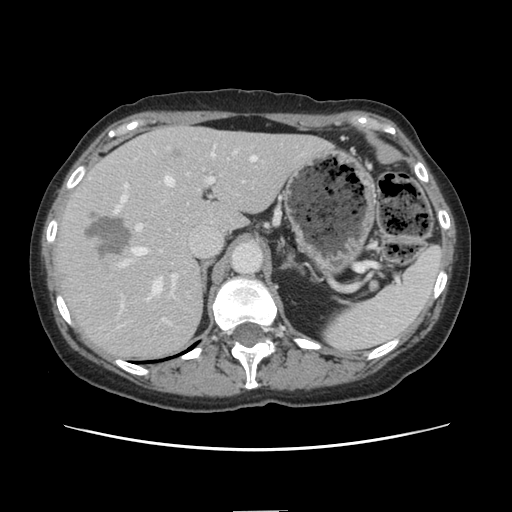
Contrast-enhanced abdominal CT, one axial slice; slice 95 of 141 in the series (ordered by position); intravenous contrast given; soft-tissue window (W 400 / L 40 HU); 2.5 mm slice thickness; 512 × 512 image matrix. Female patient, age 63 years. From the clinical record (not read from this slice): diagnosis: colorectal cancer liver metastases, imaged before liver resection; multiple liver metastases: yes; largest metastasis: 3.2 cm.
Outlined on this slice (expert manual segmentation):
- hepatic veins: bounding box [x1, y1, x2, y2] px = [123, 152, 256, 300]
- liver: [54, 128, 329, 360]
- planned liver remnant (the part of the liver to remain after resection): [183, 128, 328, 235]
- portal vein (with intrahepatic branches): [114, 149, 254, 299]